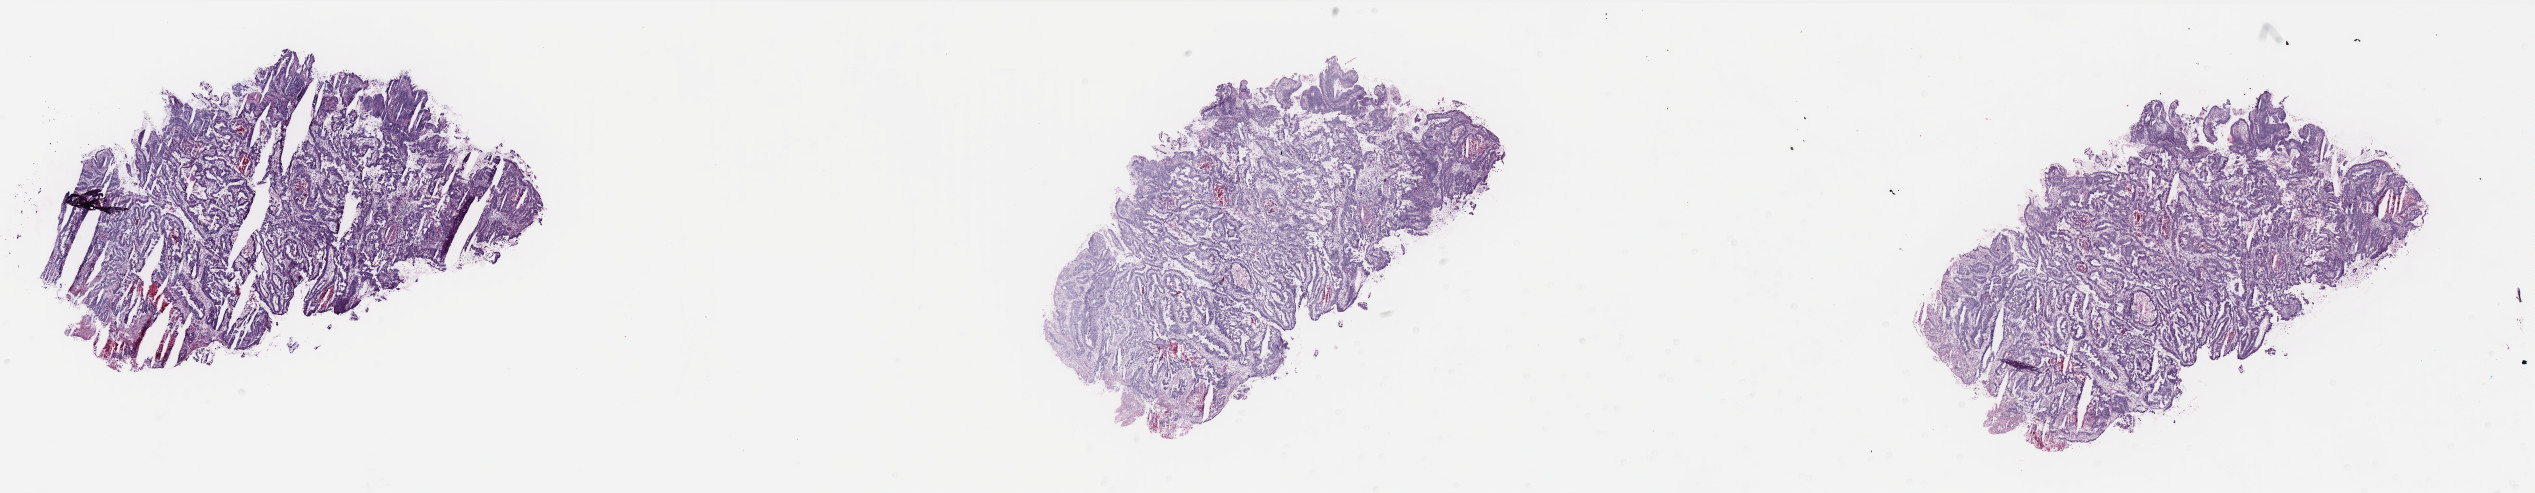
Hematoxylin and eosin (H&E) stained whole-slide image, low-resolution overview of the scanned area, about 40.6 x 7.9 mm (slide scanned at 40x); frozen section from the top of the tissue portion; sample: primary tumour, colon. Patient: male, age at initial diagnosis 66 years. Slide review estimates, as recorded: tumour cells 98%, tumour nuclei 80%, normal cells 0%, stromal cells 0%, necrosis 2%. Inflammatory infiltration, as recorded: lymphocyte infiltration 3%, monocyte infiltration 1%, neutrophil infiltration 1%.
AJCC pathologic stage: IIA. Pathologic diagnosis: Adenocarcinoma, NOS (transverse colon). TNM: T3 N0 M0. Lymph nodes positive (case pathology): 0 of 32 examined.